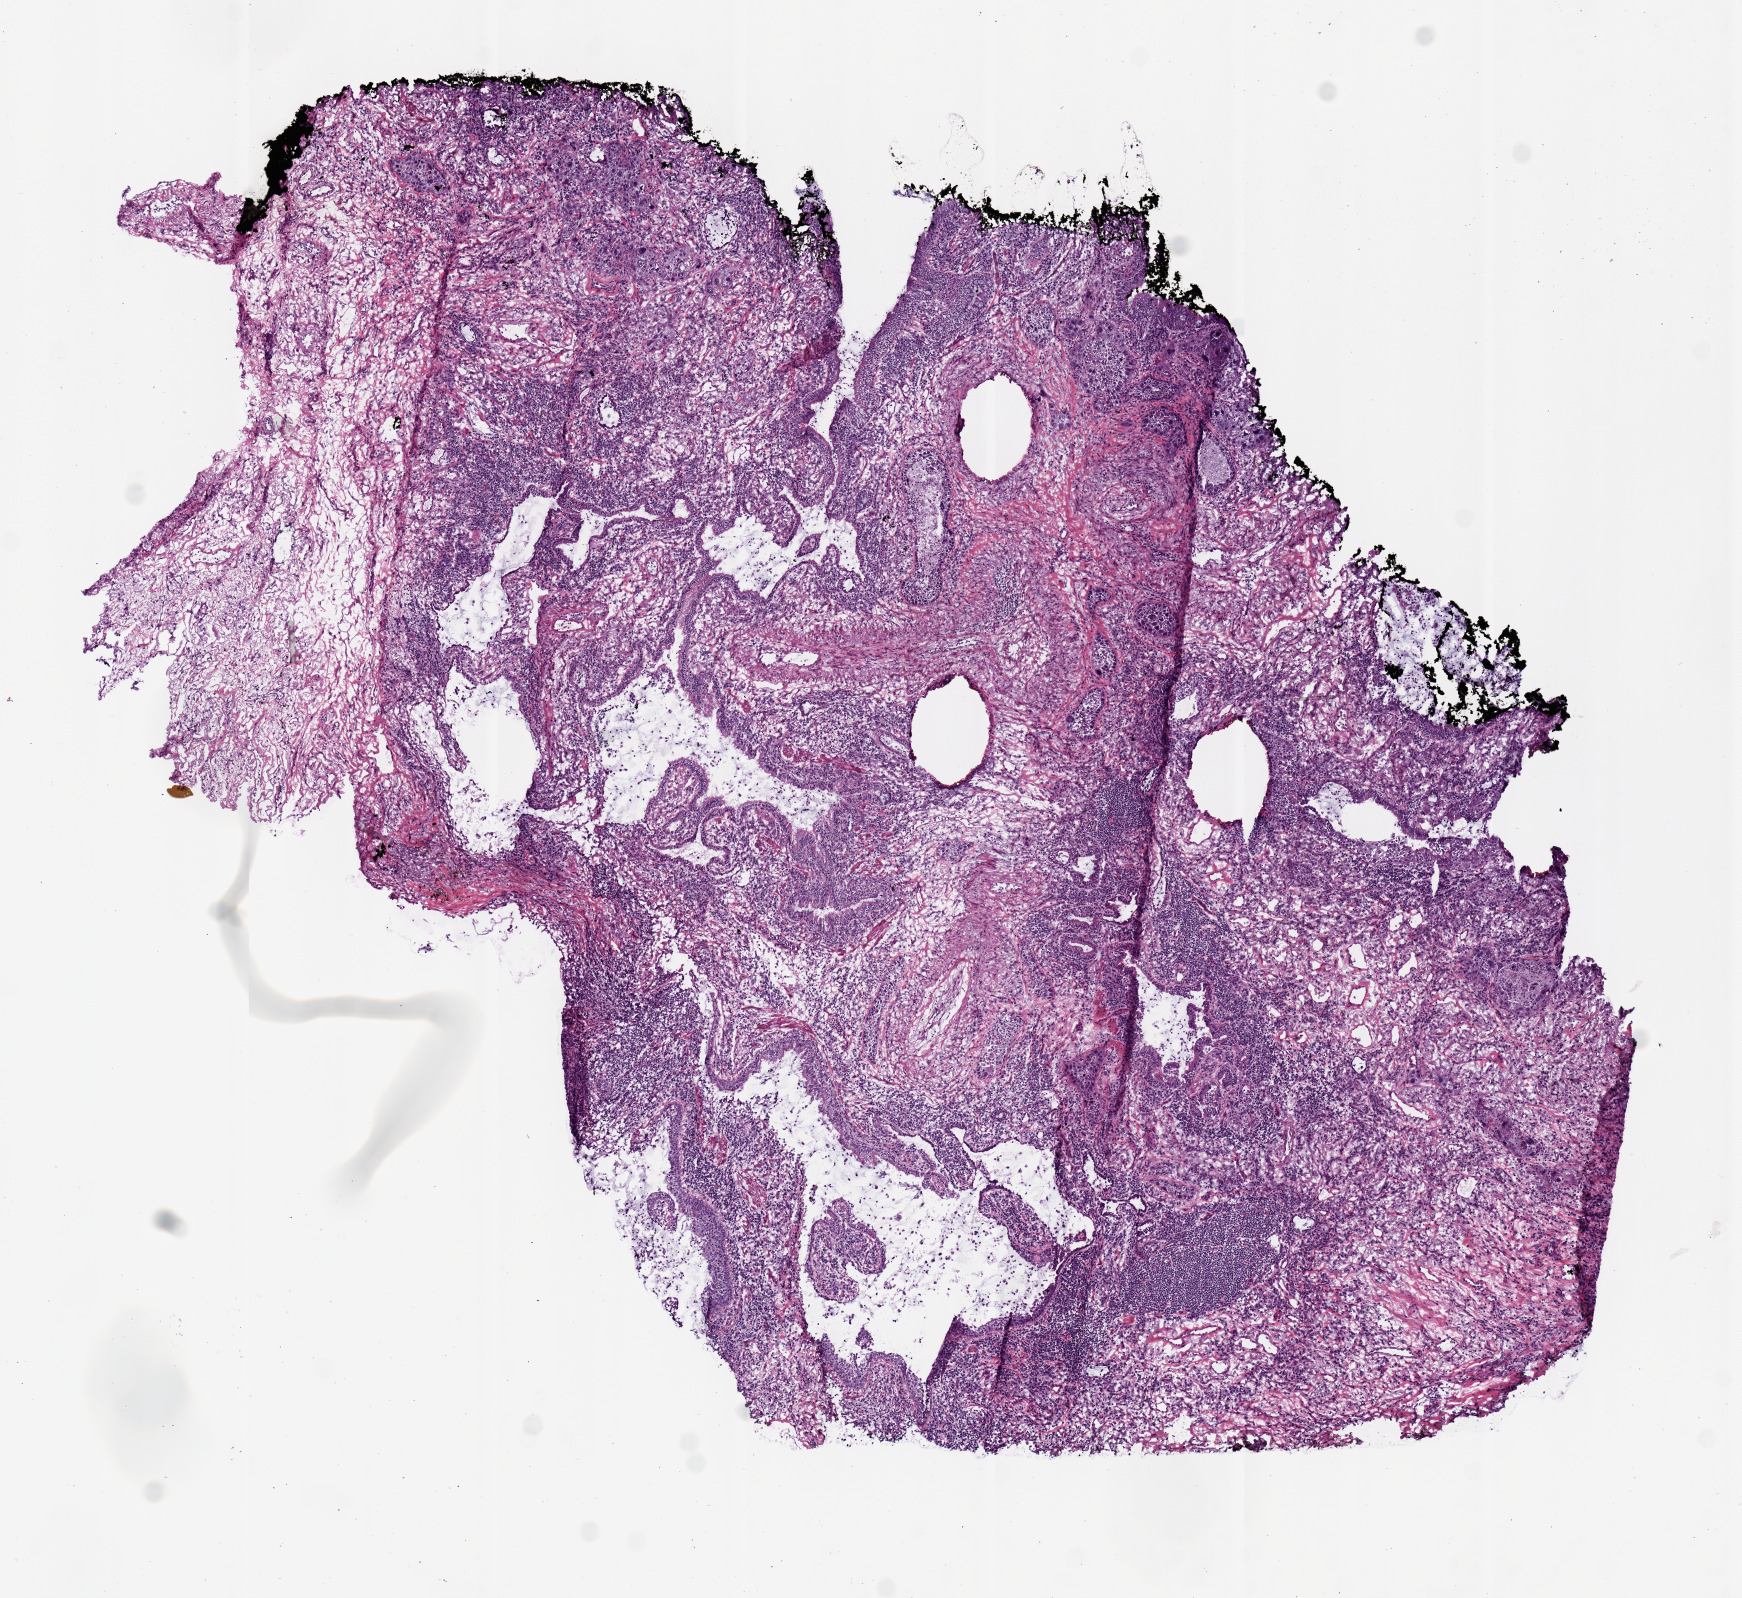
Hematoxylin and eosin (H&E) stained whole-slide image — shown as a low-resolution overview of the whole scanned area (about 6.9 x 6.3 mm, slide scanned at 20x), frozen section, lung, primary tumour sample. Female patient; age at initial diagnosis 87 years. Pathologist review of this section (percent, as recorded): tumour cells 75%, tumour nuclei 60%, normal cells 0%, stromal cells 20%, necrosis 5%.
* pathologic diagnosis: Adenocarcinoma, NOS (upper lobe, lung)
* AJCC pathologic stage: IB (7th edition)